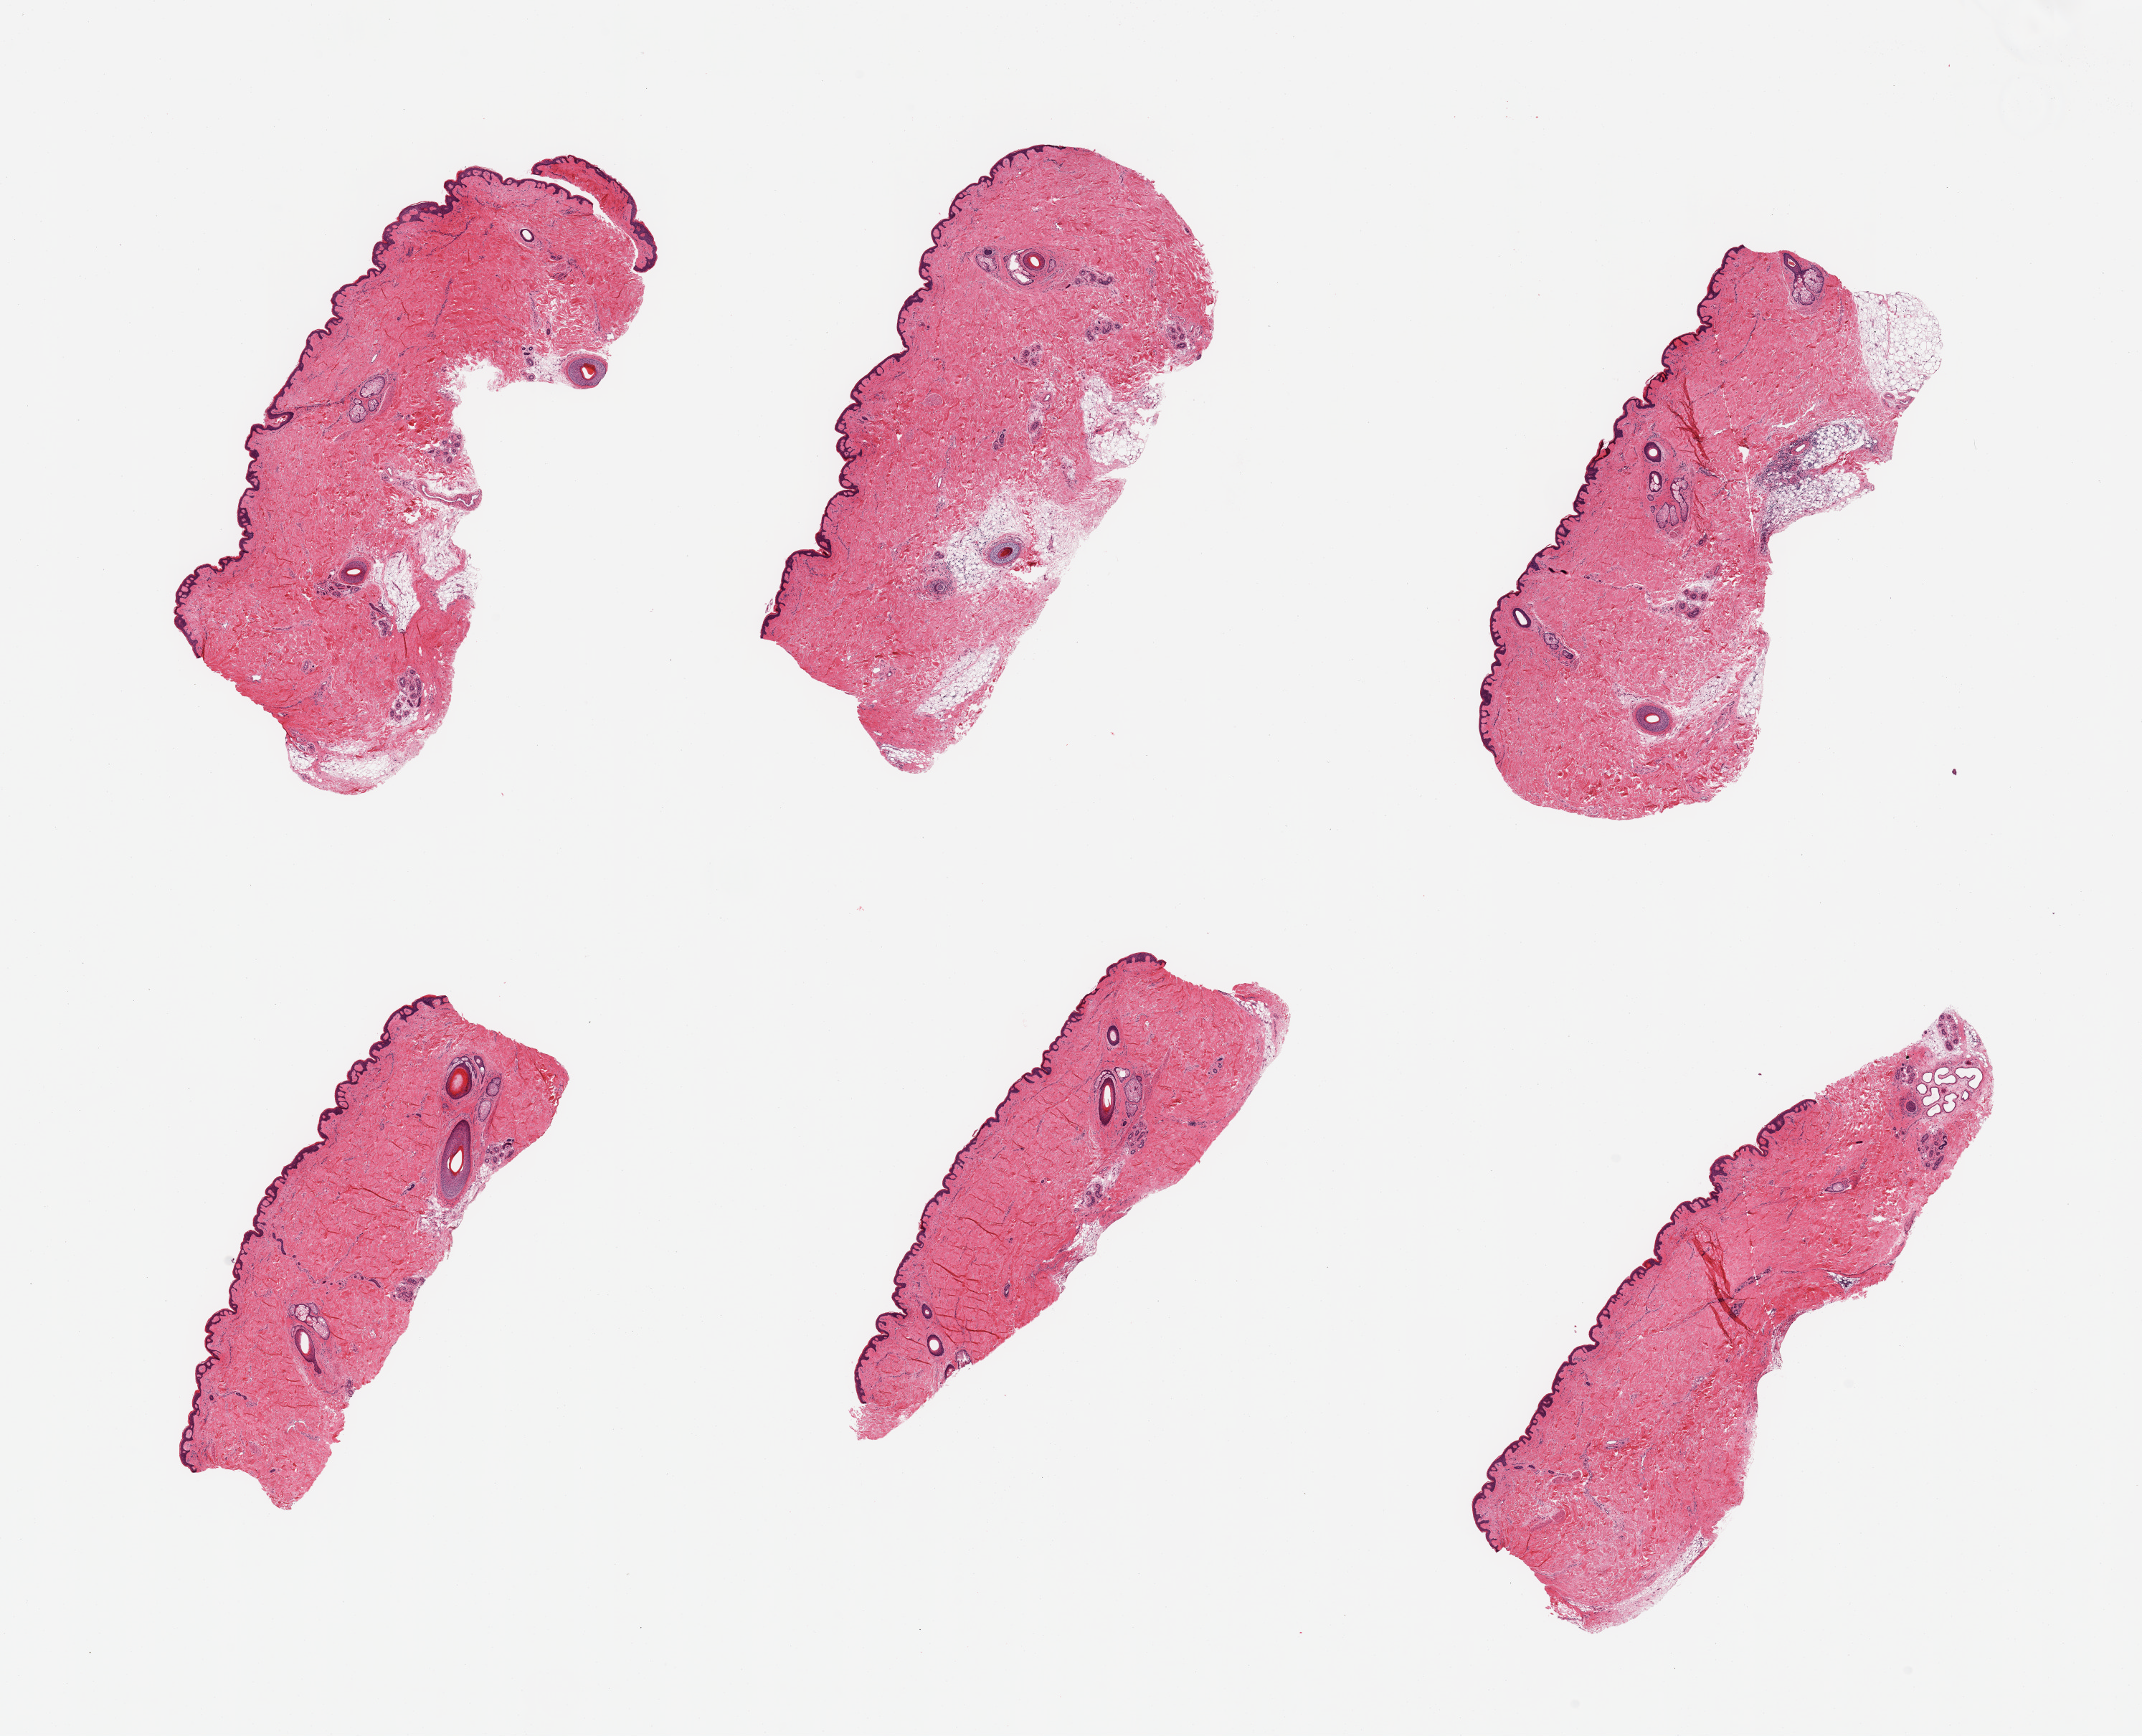
Digitized hematoxylin and eosin (H&E)-stained section, whole scanned area (about 23.6 x 19.1 mm, slide scanned at 20x) shown as a low-resolution overview; PAXgene-fixed paraffin-embedded (PFPE) section; section of skin of suprapubic region (target tissue); donor tissue sample. Donor sex: male.
* pathologist's review note for this sample: 6 pieces; few pieces include ~10% adherent fat with focal lymphoid infiltrate